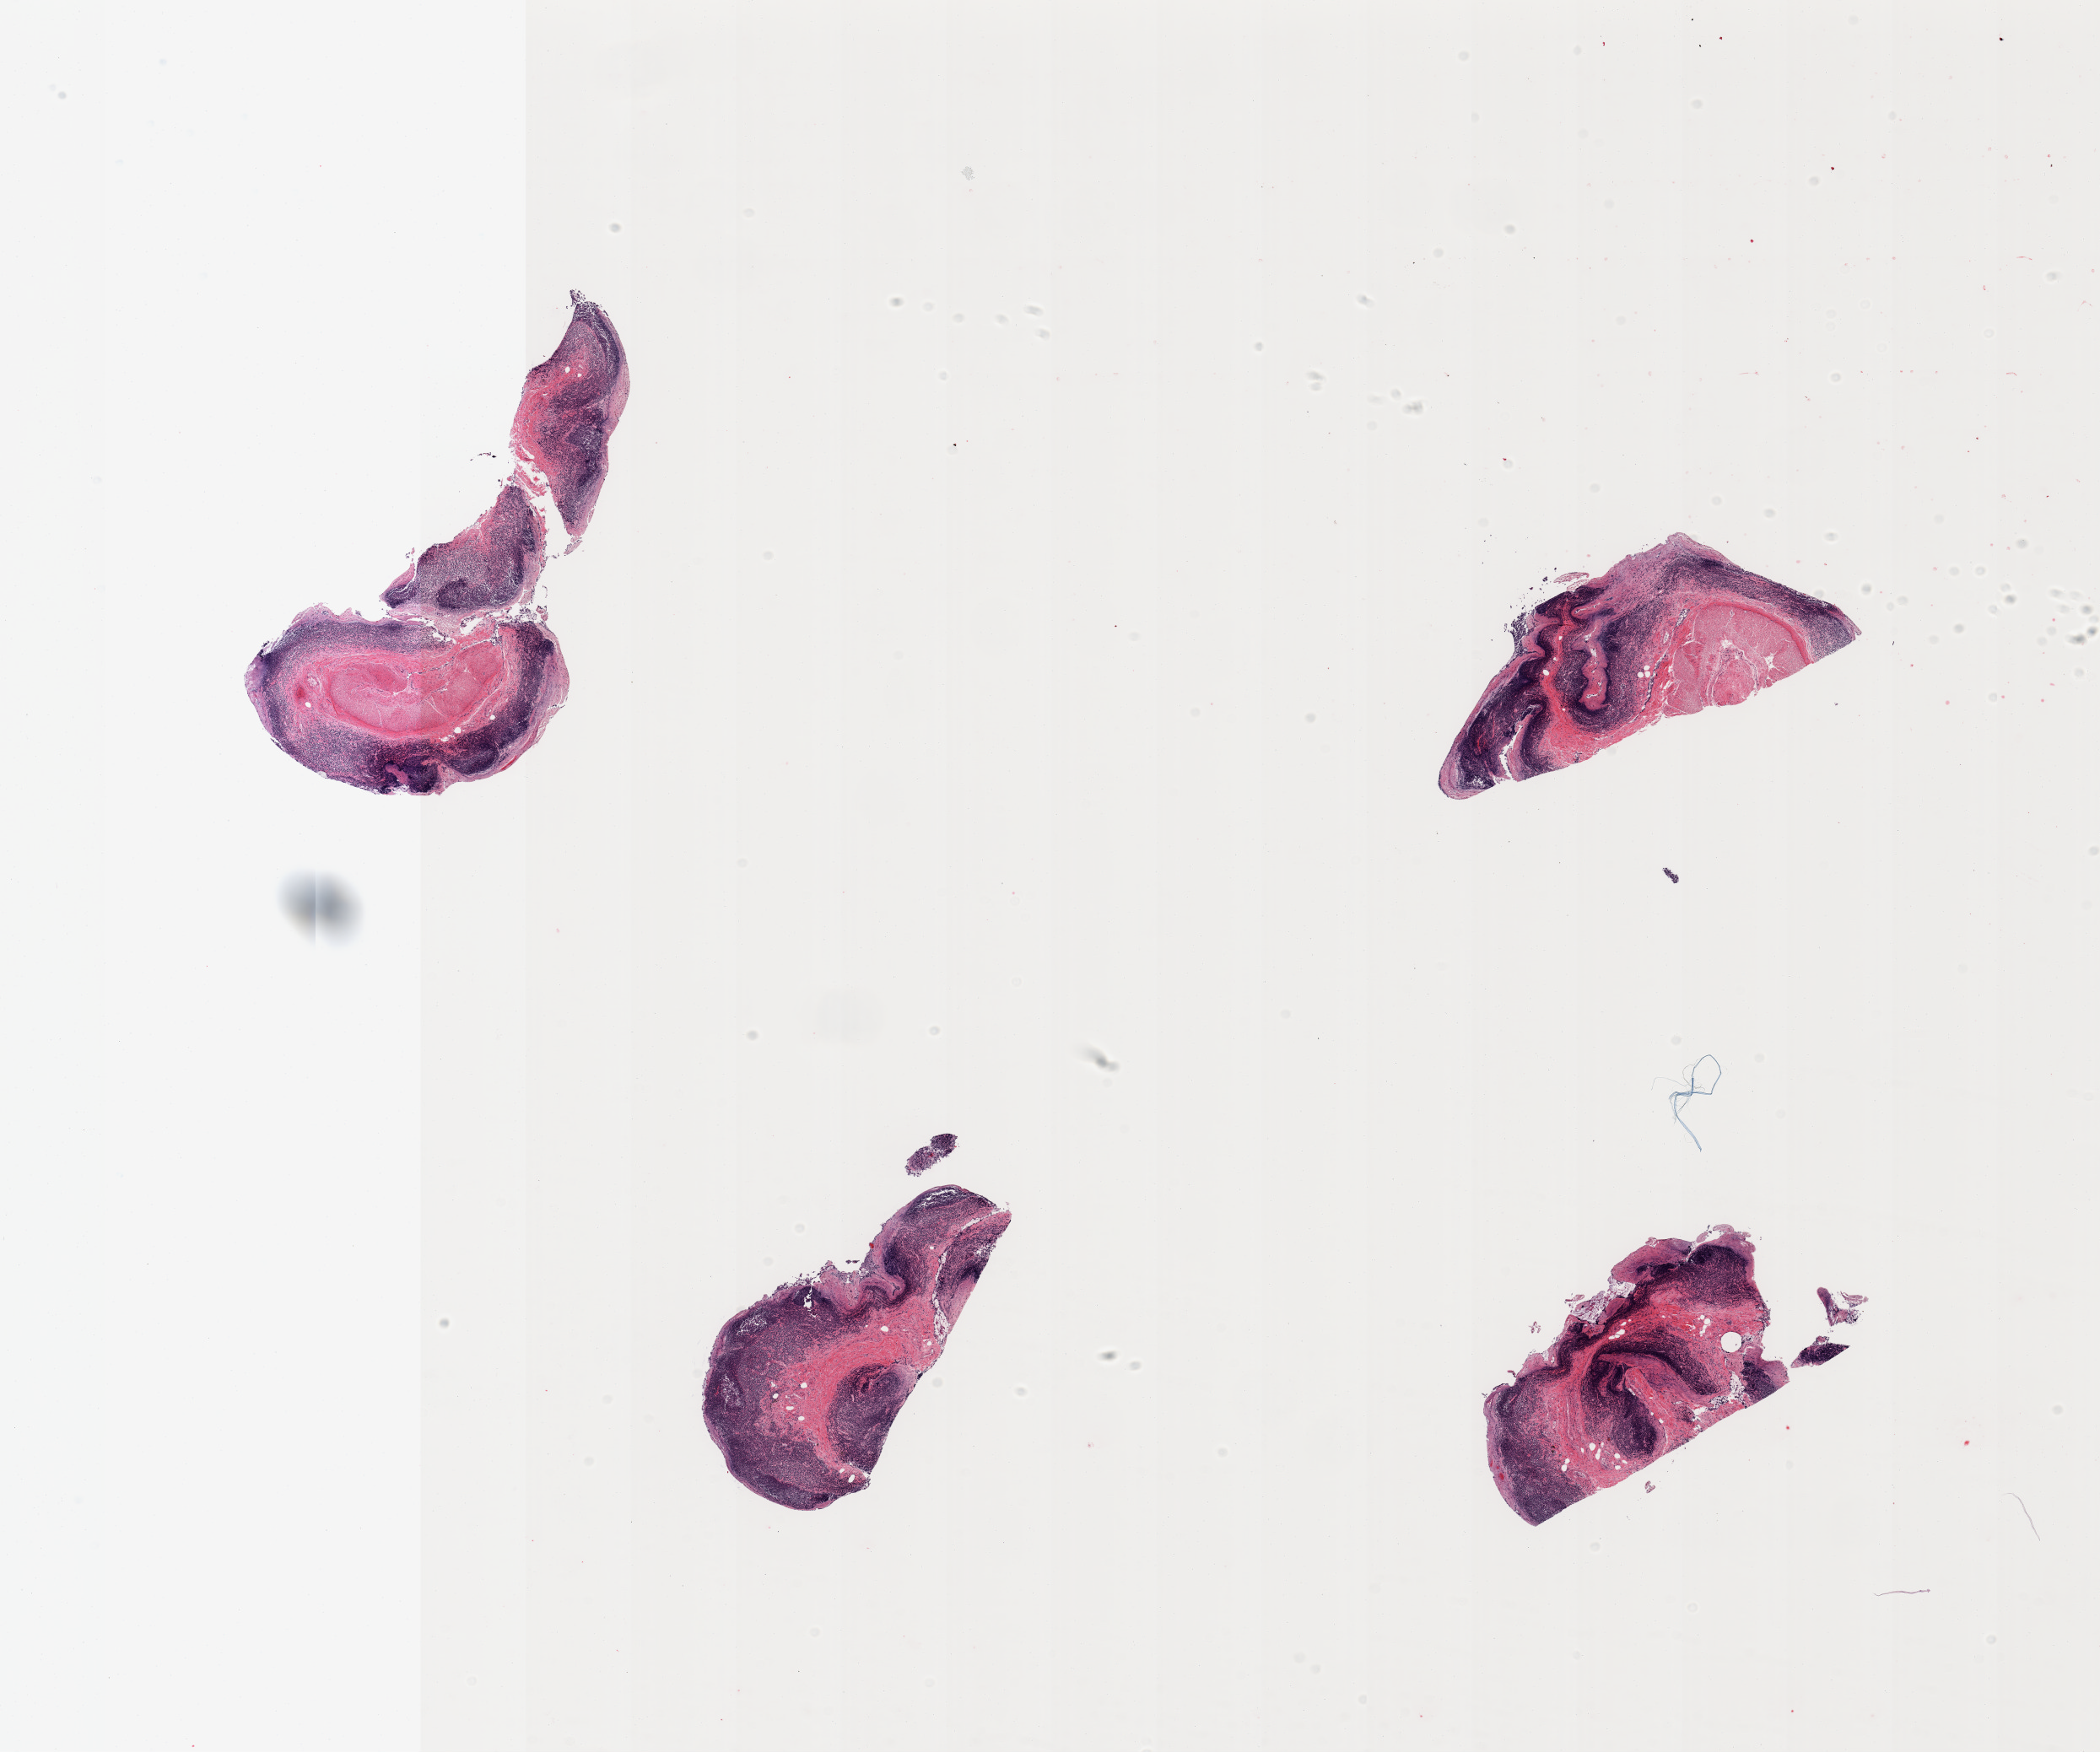
Whole-slide image, haematoxylin and eosin stain — whole scanned area (about 19.7 x 16.4 mm, acquisition: 20x scan) shown as a low-resolution overview; PAXgene-fixed, paraffin-embedded tissue; sampled site (target tissue): ileum; donor tissue sample. Donor: male.
• pathologist's review note for this sample: 4 pieces; abundant but moderately autolyzed lymphoid tissue; muscle in 2 of 4